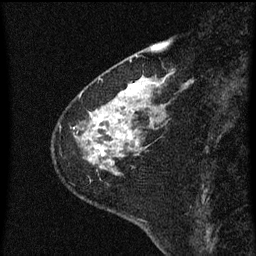
Breast MRI (dynamic contrast-enhanced), one sagittal slice; position 16 of 60 along the scan axis; dynamic contrast-enhanced series, image 2 of 3 at this slice position (ordered by acquisition); 1.5 T; TE 4.2 ms, TR 8 ms; 256 × 256 image matrix, field of view 180 × 180 mm. Female patient, age 60 years.
Annotated regions visible in this slice (semi-automatic segmentation, software-assisted and operator-edited):
- analysis volume of interest (the breast-tissue region the enhancement analysis was run in; not a lesion): bounding box [x1, y1, x2, y2] px = [62, 82, 159, 183]
- tumour enhancement mask (voxels above the 70 % enhancement threshold inside the analysis volume of interest): [94, 84, 140, 157]